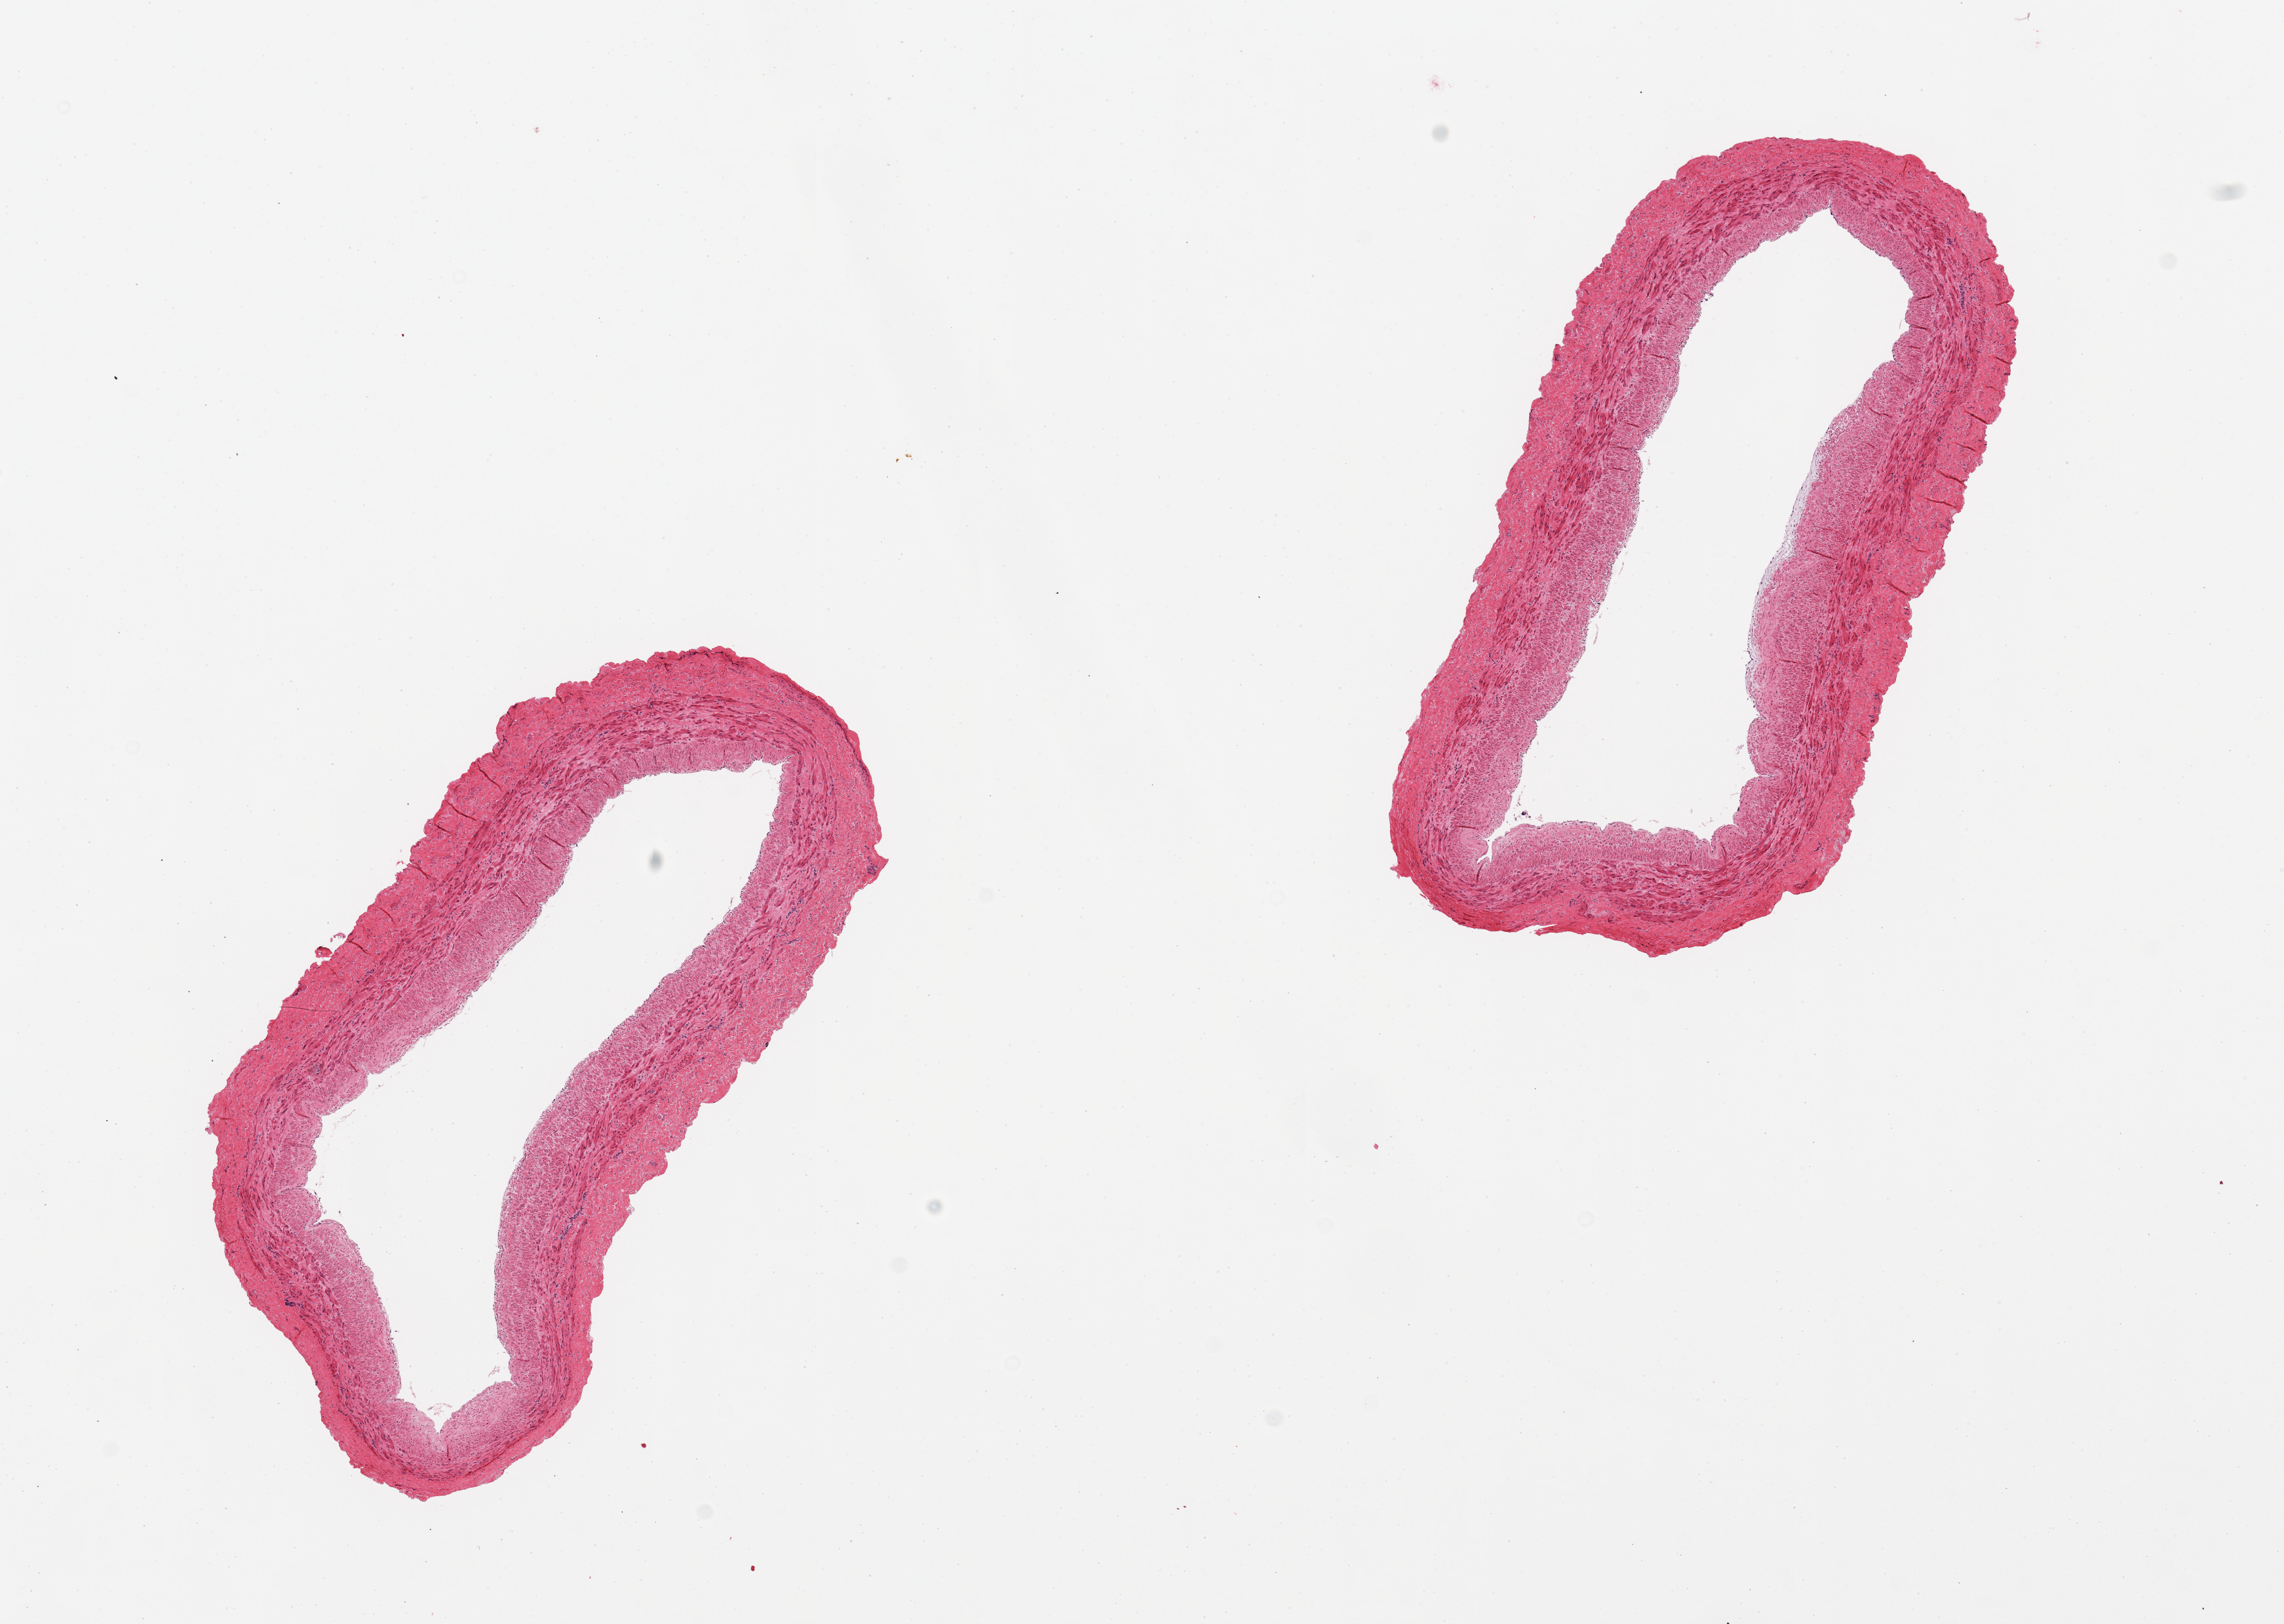
Digitized hematoxylin and eosin (H&E)-stained section, a low-resolution overview of the entire scanned area, about 13.8 x 9.8 mm (slide scanned at 20x), PAXgene-fixed paraffin-embedded (PFPE) section, target tissue: tibial artery, donor tissue sample. Donor: female.
Pathologist's review note for this sample: 2 pieces, no adherent fat or atherosis.